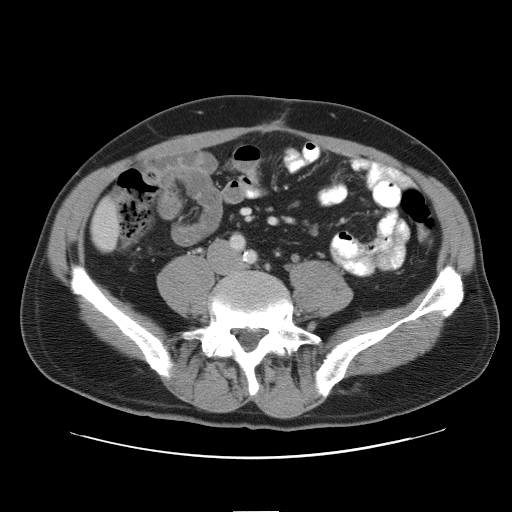
Contrast-enhanced abdominal CT, one axial slice. Slice 8 of 52 in the series (ordered by position). Reconstruction kernel STANDARD. 120 kVp. Intravenous contrast given. Soft-tissue window (W 400 / L 40 HU). 5 mm slice thickness. 512 × 512 image matrix. Male patient, age 70 years. From the clinical record (not read from this slice): diagnosis: colorectal cancer liver metastases, imaged before liver resection; multiple liver metastases: yes; largest metastasis: 4 cm; disease in both lobes: yes.
Outlined on this slice (outlined manually by an expert reader):
- liver: bounding box <91,199,119,251> (left, top, right, bottom; pixels)